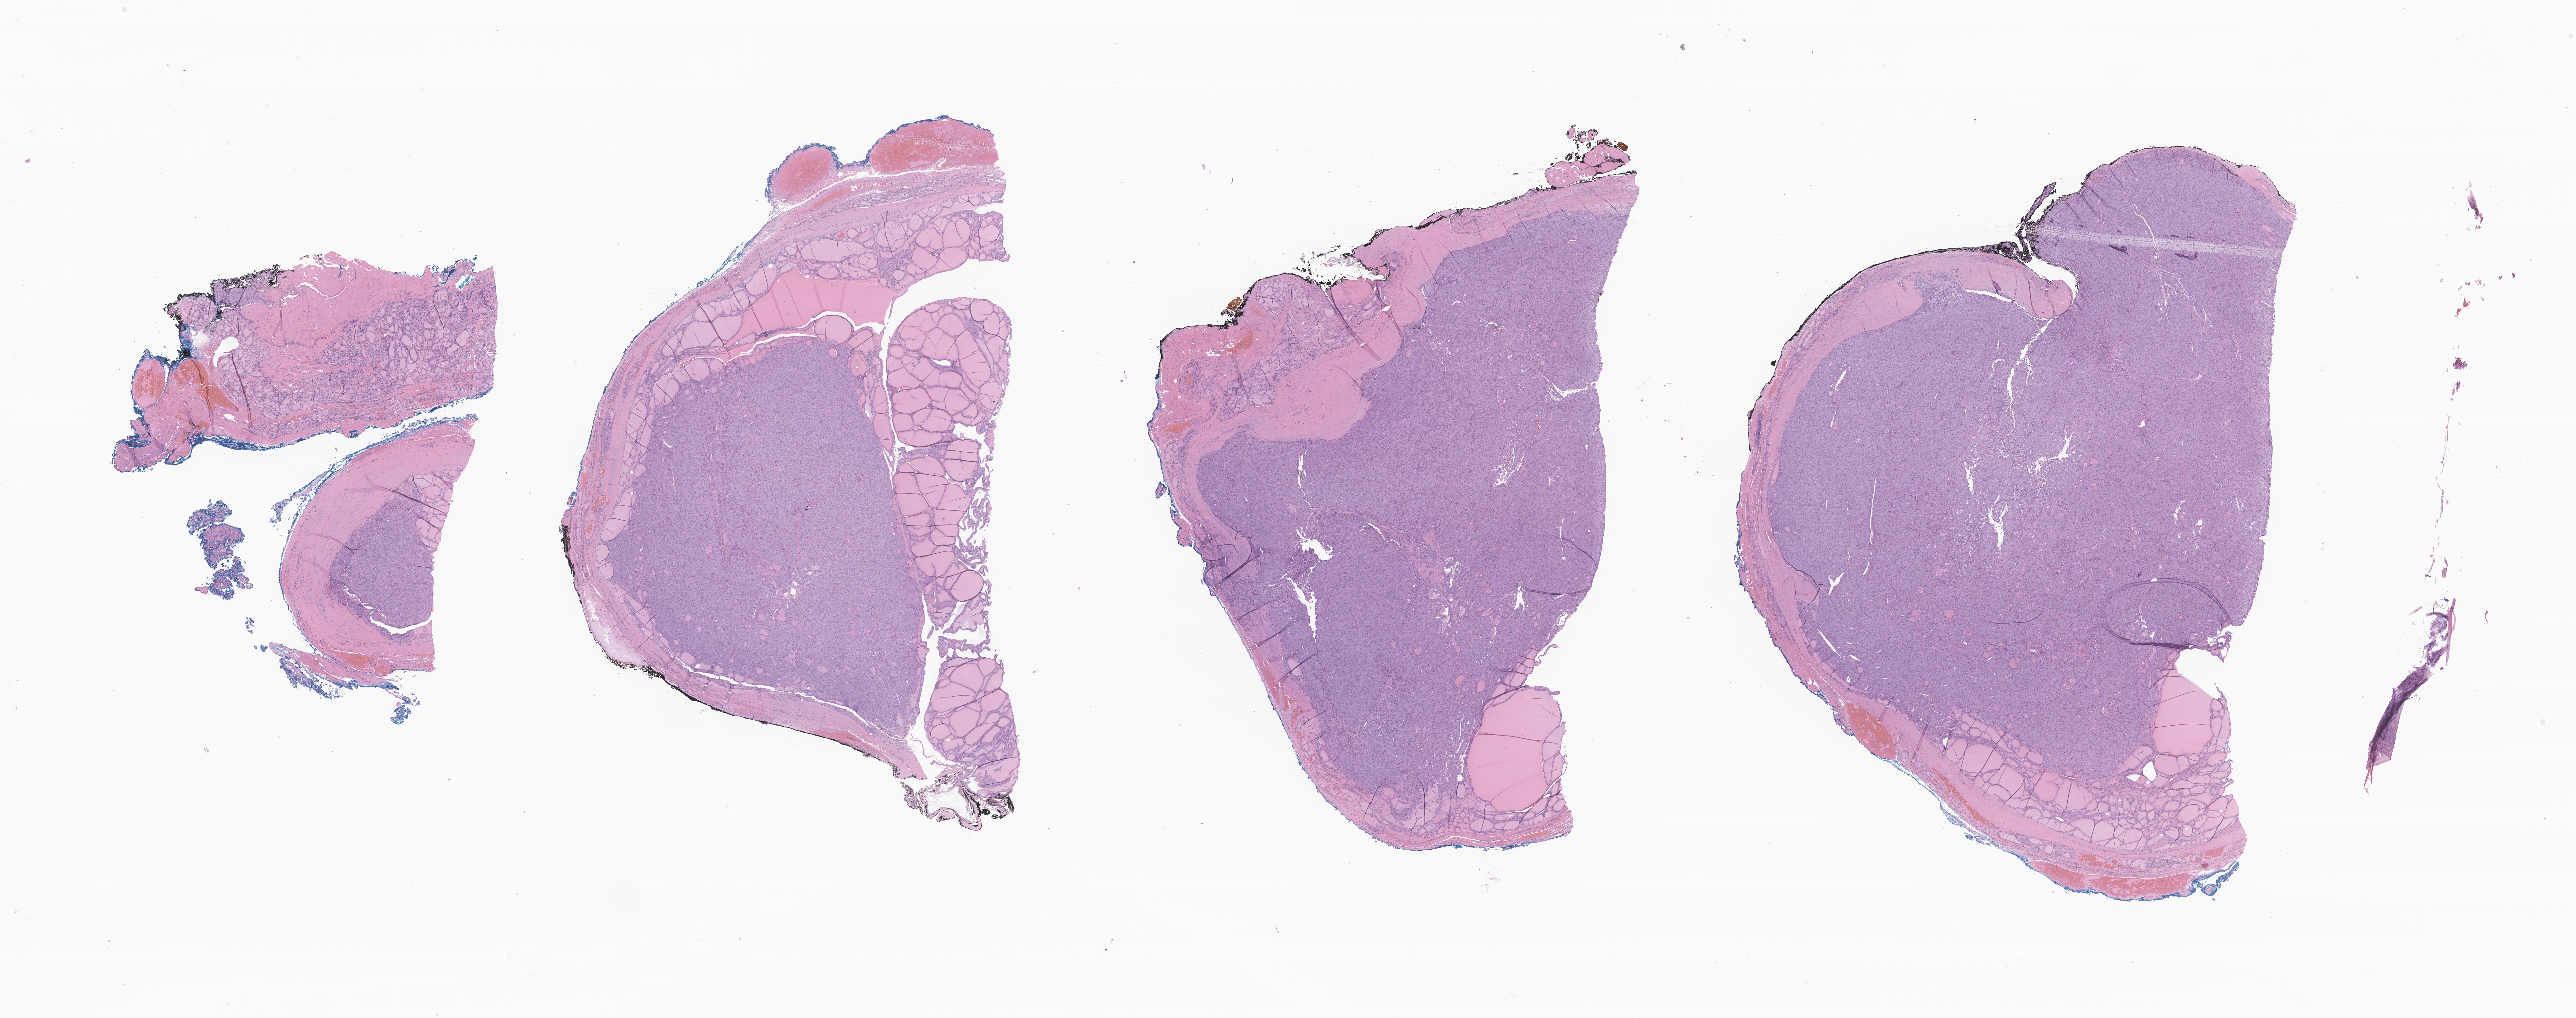
Whole-slide image, haematoxylin and eosin stain of tumor tissue from the thyroid, whole scanned area (about 41.2 x 16.3 mm) shown as a low-resolution overview; FFPE section. Female patient, age 119 months (9 years 11 months).
Recorded diagnosis: Papillary carcinoma, encapsulated, of thyroid.